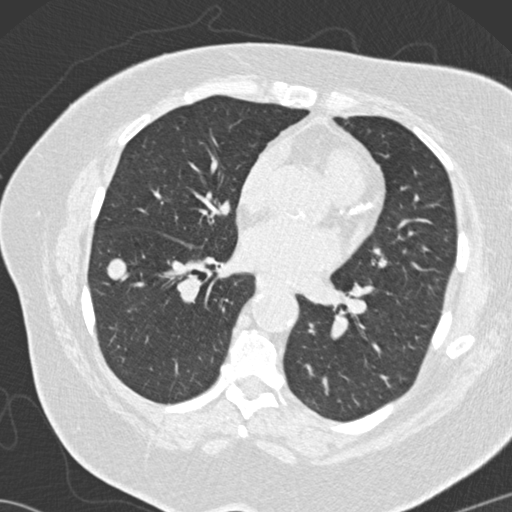
Low-dose screening chest CT, one axial slice; position 65 of 146 along the scan axis; reconstruction kernel B30f; 120 kVp; lung window (W 1500 / L -600 HU); 2 mm slice thickness; 512 × 512 image matrix, field of view 350 × 350 mm.
Annotated regions visible in this slice (expert manual segmentation):
- lesion 2 (tumor, lower lobe of right lung): bounding box <107,259,127,279> (left, top, right, bottom; pixels)